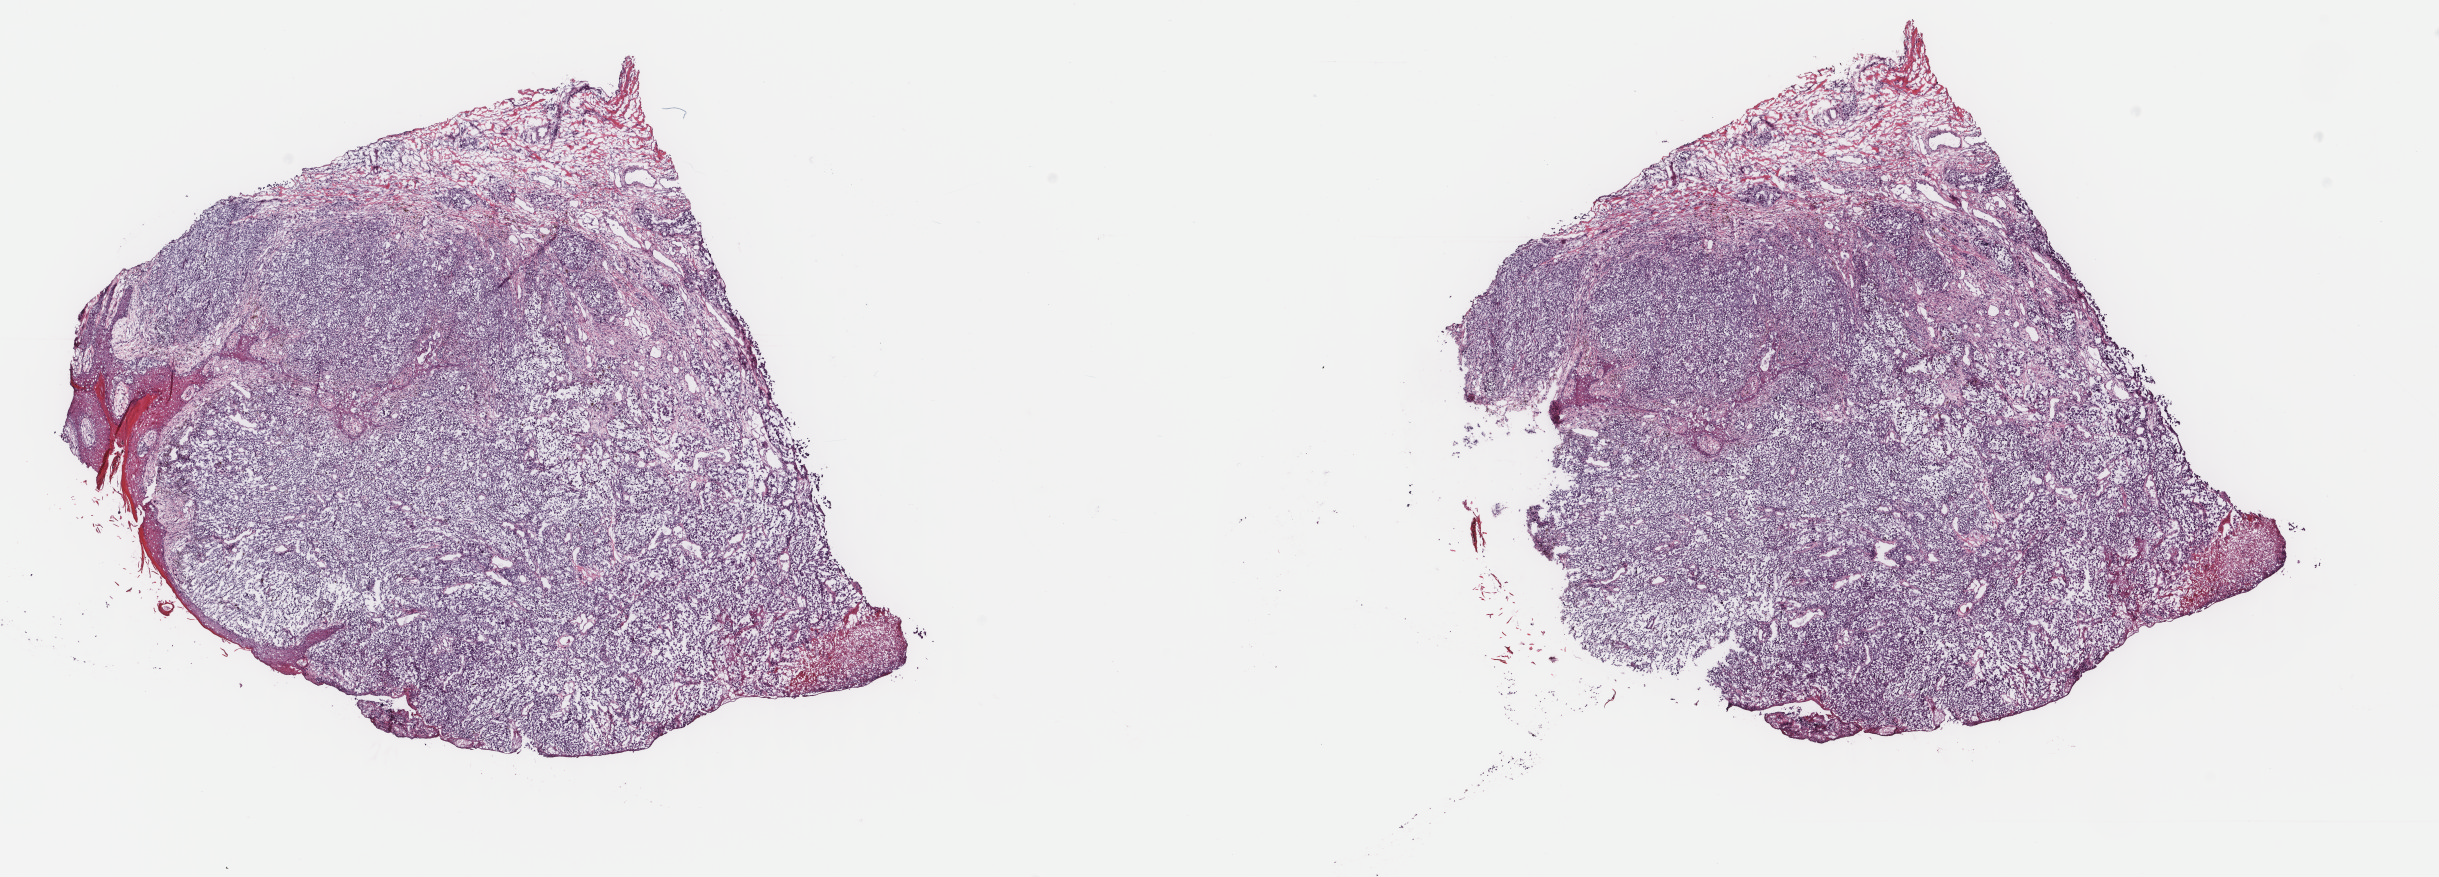
Hematoxylin and eosin (H&E) stained whole-slide image, whole scanned area (about 19.4 x 7.0 mm, slide scanned at 40x) shown as a low-resolution overview. Frozen section from the top of the tissue portion. Skin, primary tumour sample. Female, age 81 years at initial diagnosis. Composition of this section per pathologist review: tumour cells 95%, tumour nuclei 85%, normal cells 0%, stromal cells 5%, necrosis 0%. Inflammatory infiltration, as recorded: lymphocyte infiltration 0%, monocyte infiltration 0%, neutrophil infiltration 0%.
* pathologic diagnosis: Malignant melanoma, NOS
* AJCC pathologic stage: IIIC